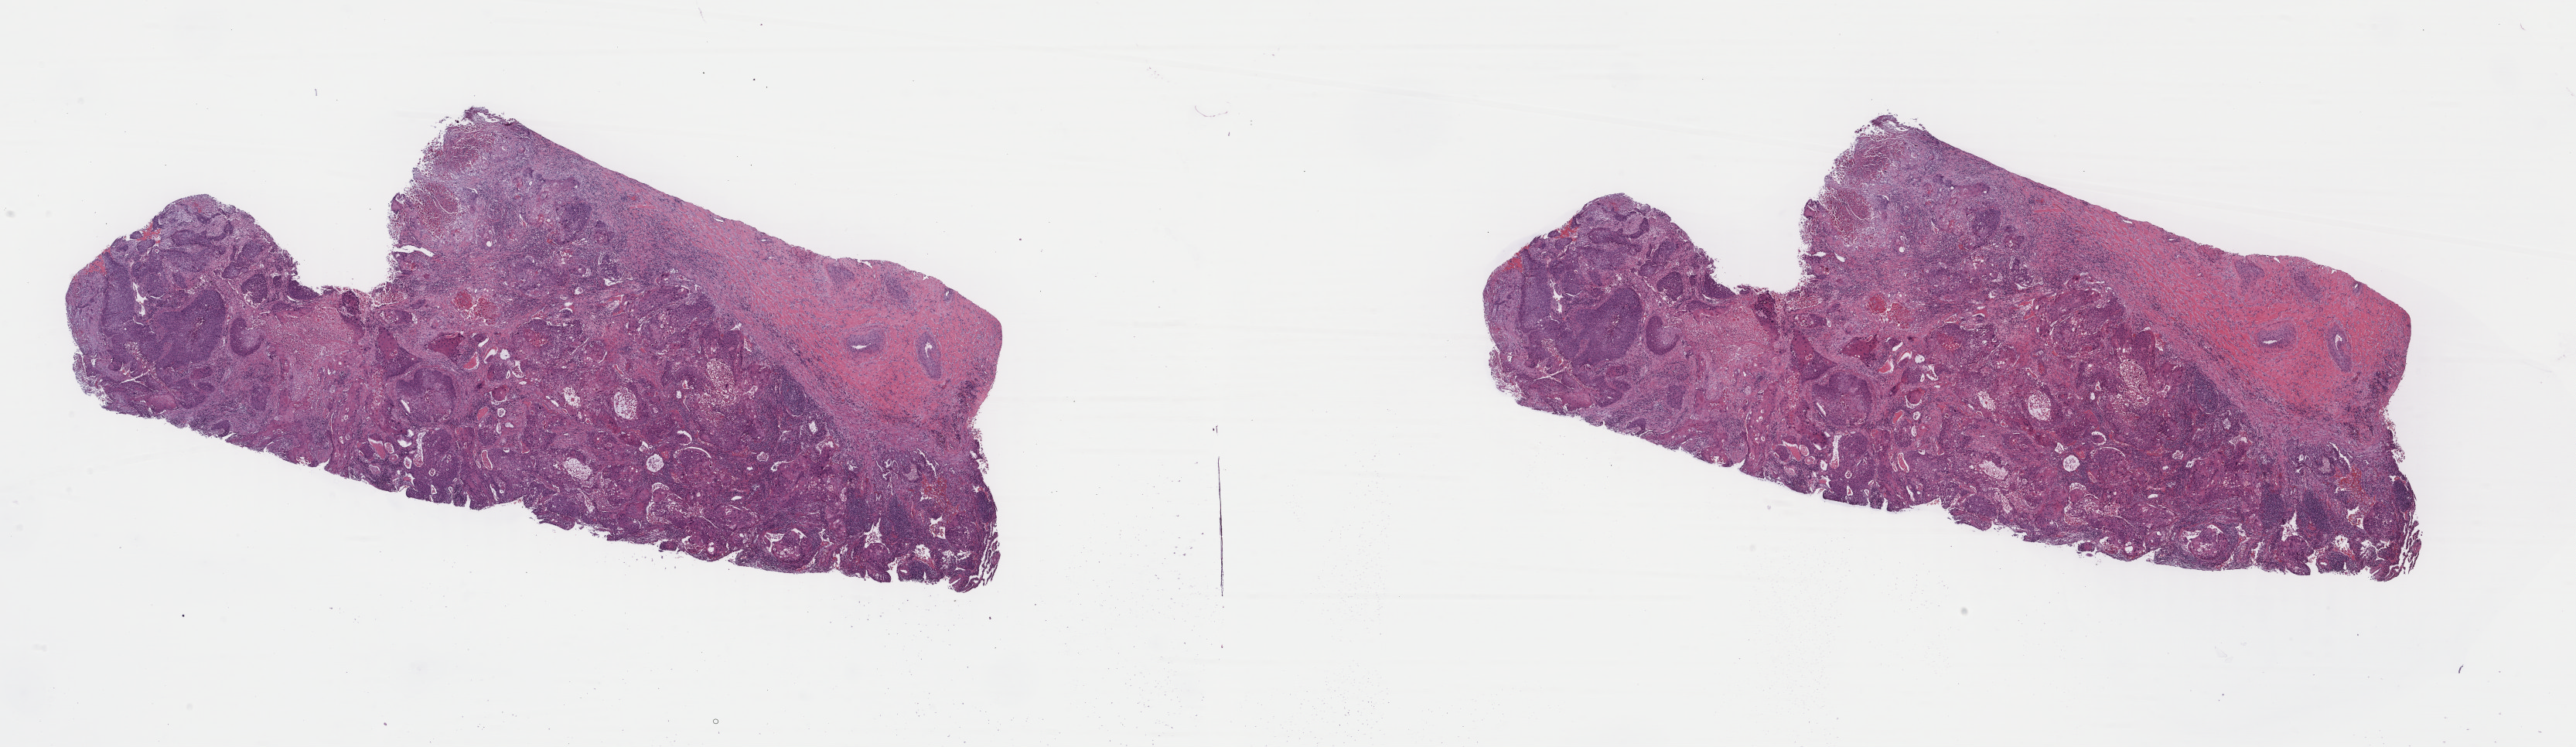
Whole-slide histology image, H&E, whole scanned area (about 26.4 x 7.7 mm, from a 40x scan) shown as a low-resolution overview. Formalin-fixed paraffin-embedded (FFPE) diagnostic section. Primary tumour sample from the lung. Patient: male, age at initial diagnosis 61 years.
Laterality: right. AJCC pathologic stage: IIIA (7th edition). Diagnosis: Squamous cell carcinoma, NOS. TNM: T2a N2 M0.